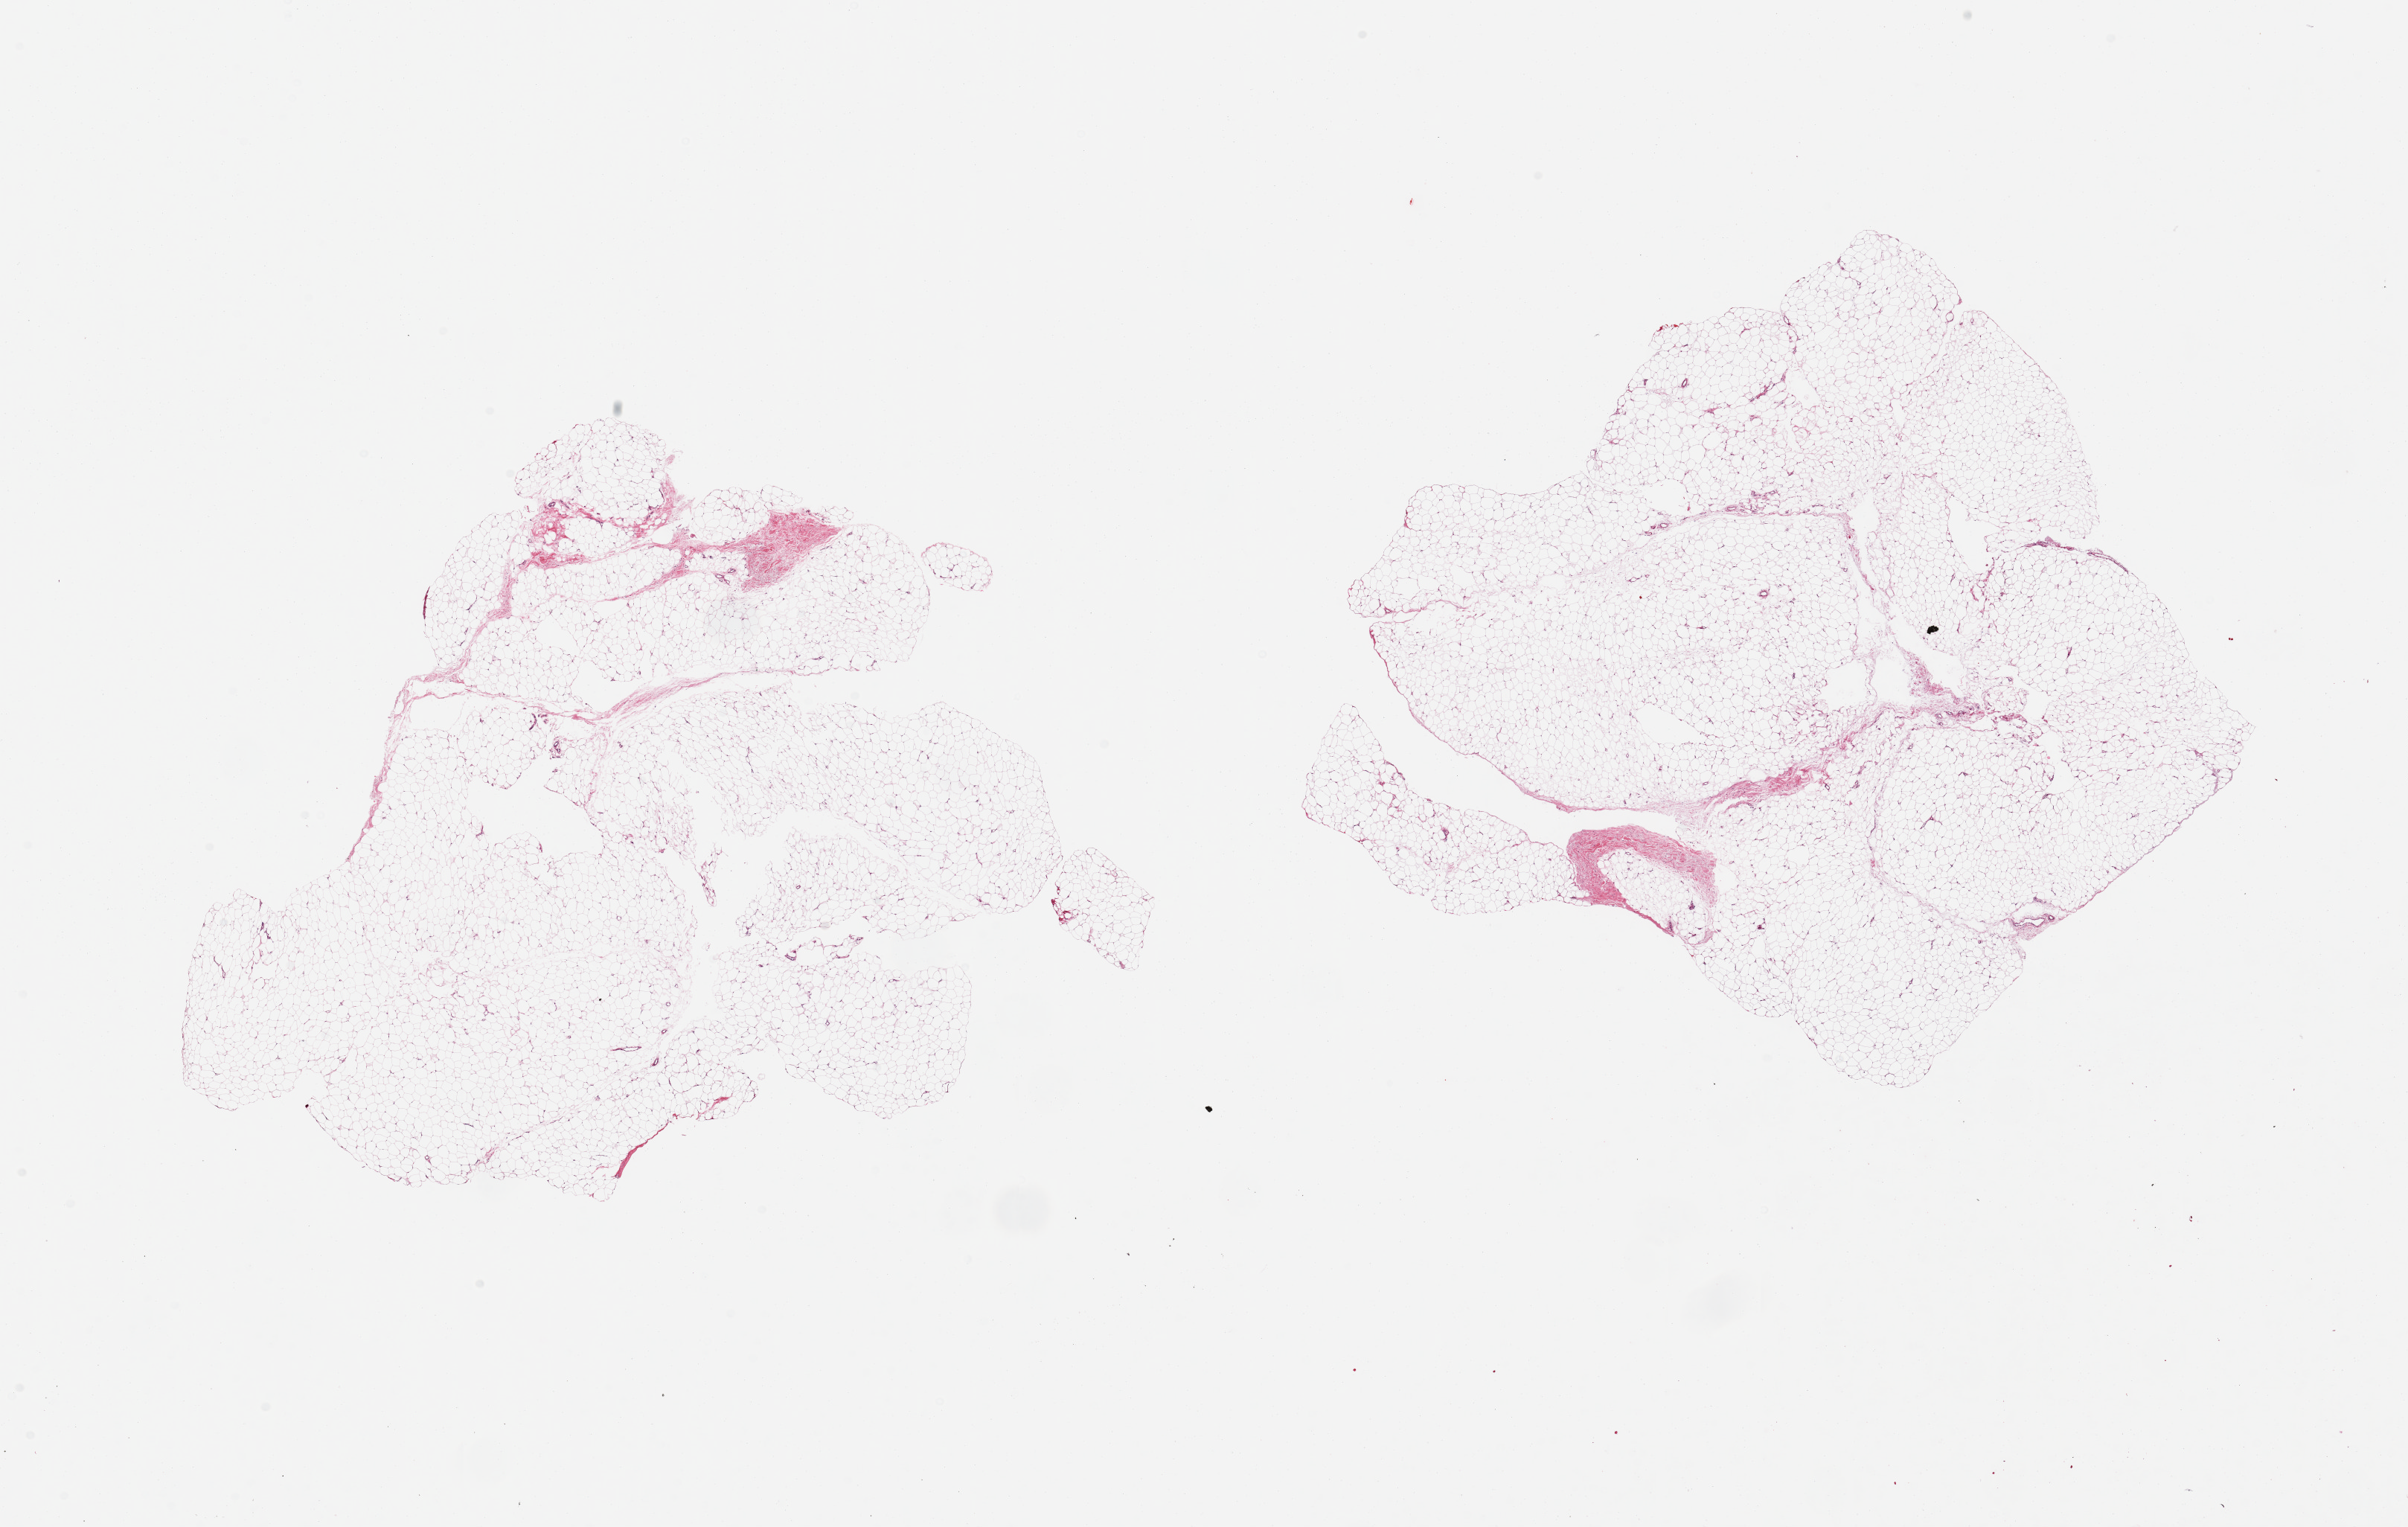
Digitized hematoxylin and eosin (H&E)-stained section, a low-resolution overview of the entire scanned area, about 25.6 x 16.2 mm (acquisition: 20x scan), PAXgene-fixed paraffin-embedded (PFPE) section, section of adipose tissue (target tissue), tissue donor sample. Donor sex: female.
Pathologist's review note for this sample: 2 pieces; mature adipose tissue with trace of fibrovascular component.